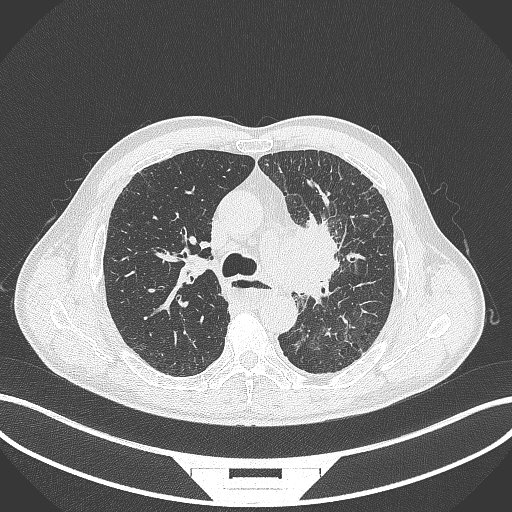
Chest CT, one axial slice; slice 255 of 411 in the series (ordered by position); lung window (W 1500 / L -600 HU); 1 mm slice thickness; 512 × 512 image matrix, field of view 400 × 400 mm. Patient: male, 57 years. Case-level facts recorded for this patient, not image findings: clinical TNM (as recorded): T2a N1 M0.
Annotated regions visible in this slice (bounding box drawn by a radiologist):
- lung tumour (recorded histology: squamous cell carcinoma): bounding box (x1, y1, x2, y2) in pixels: (273, 214, 348, 310)